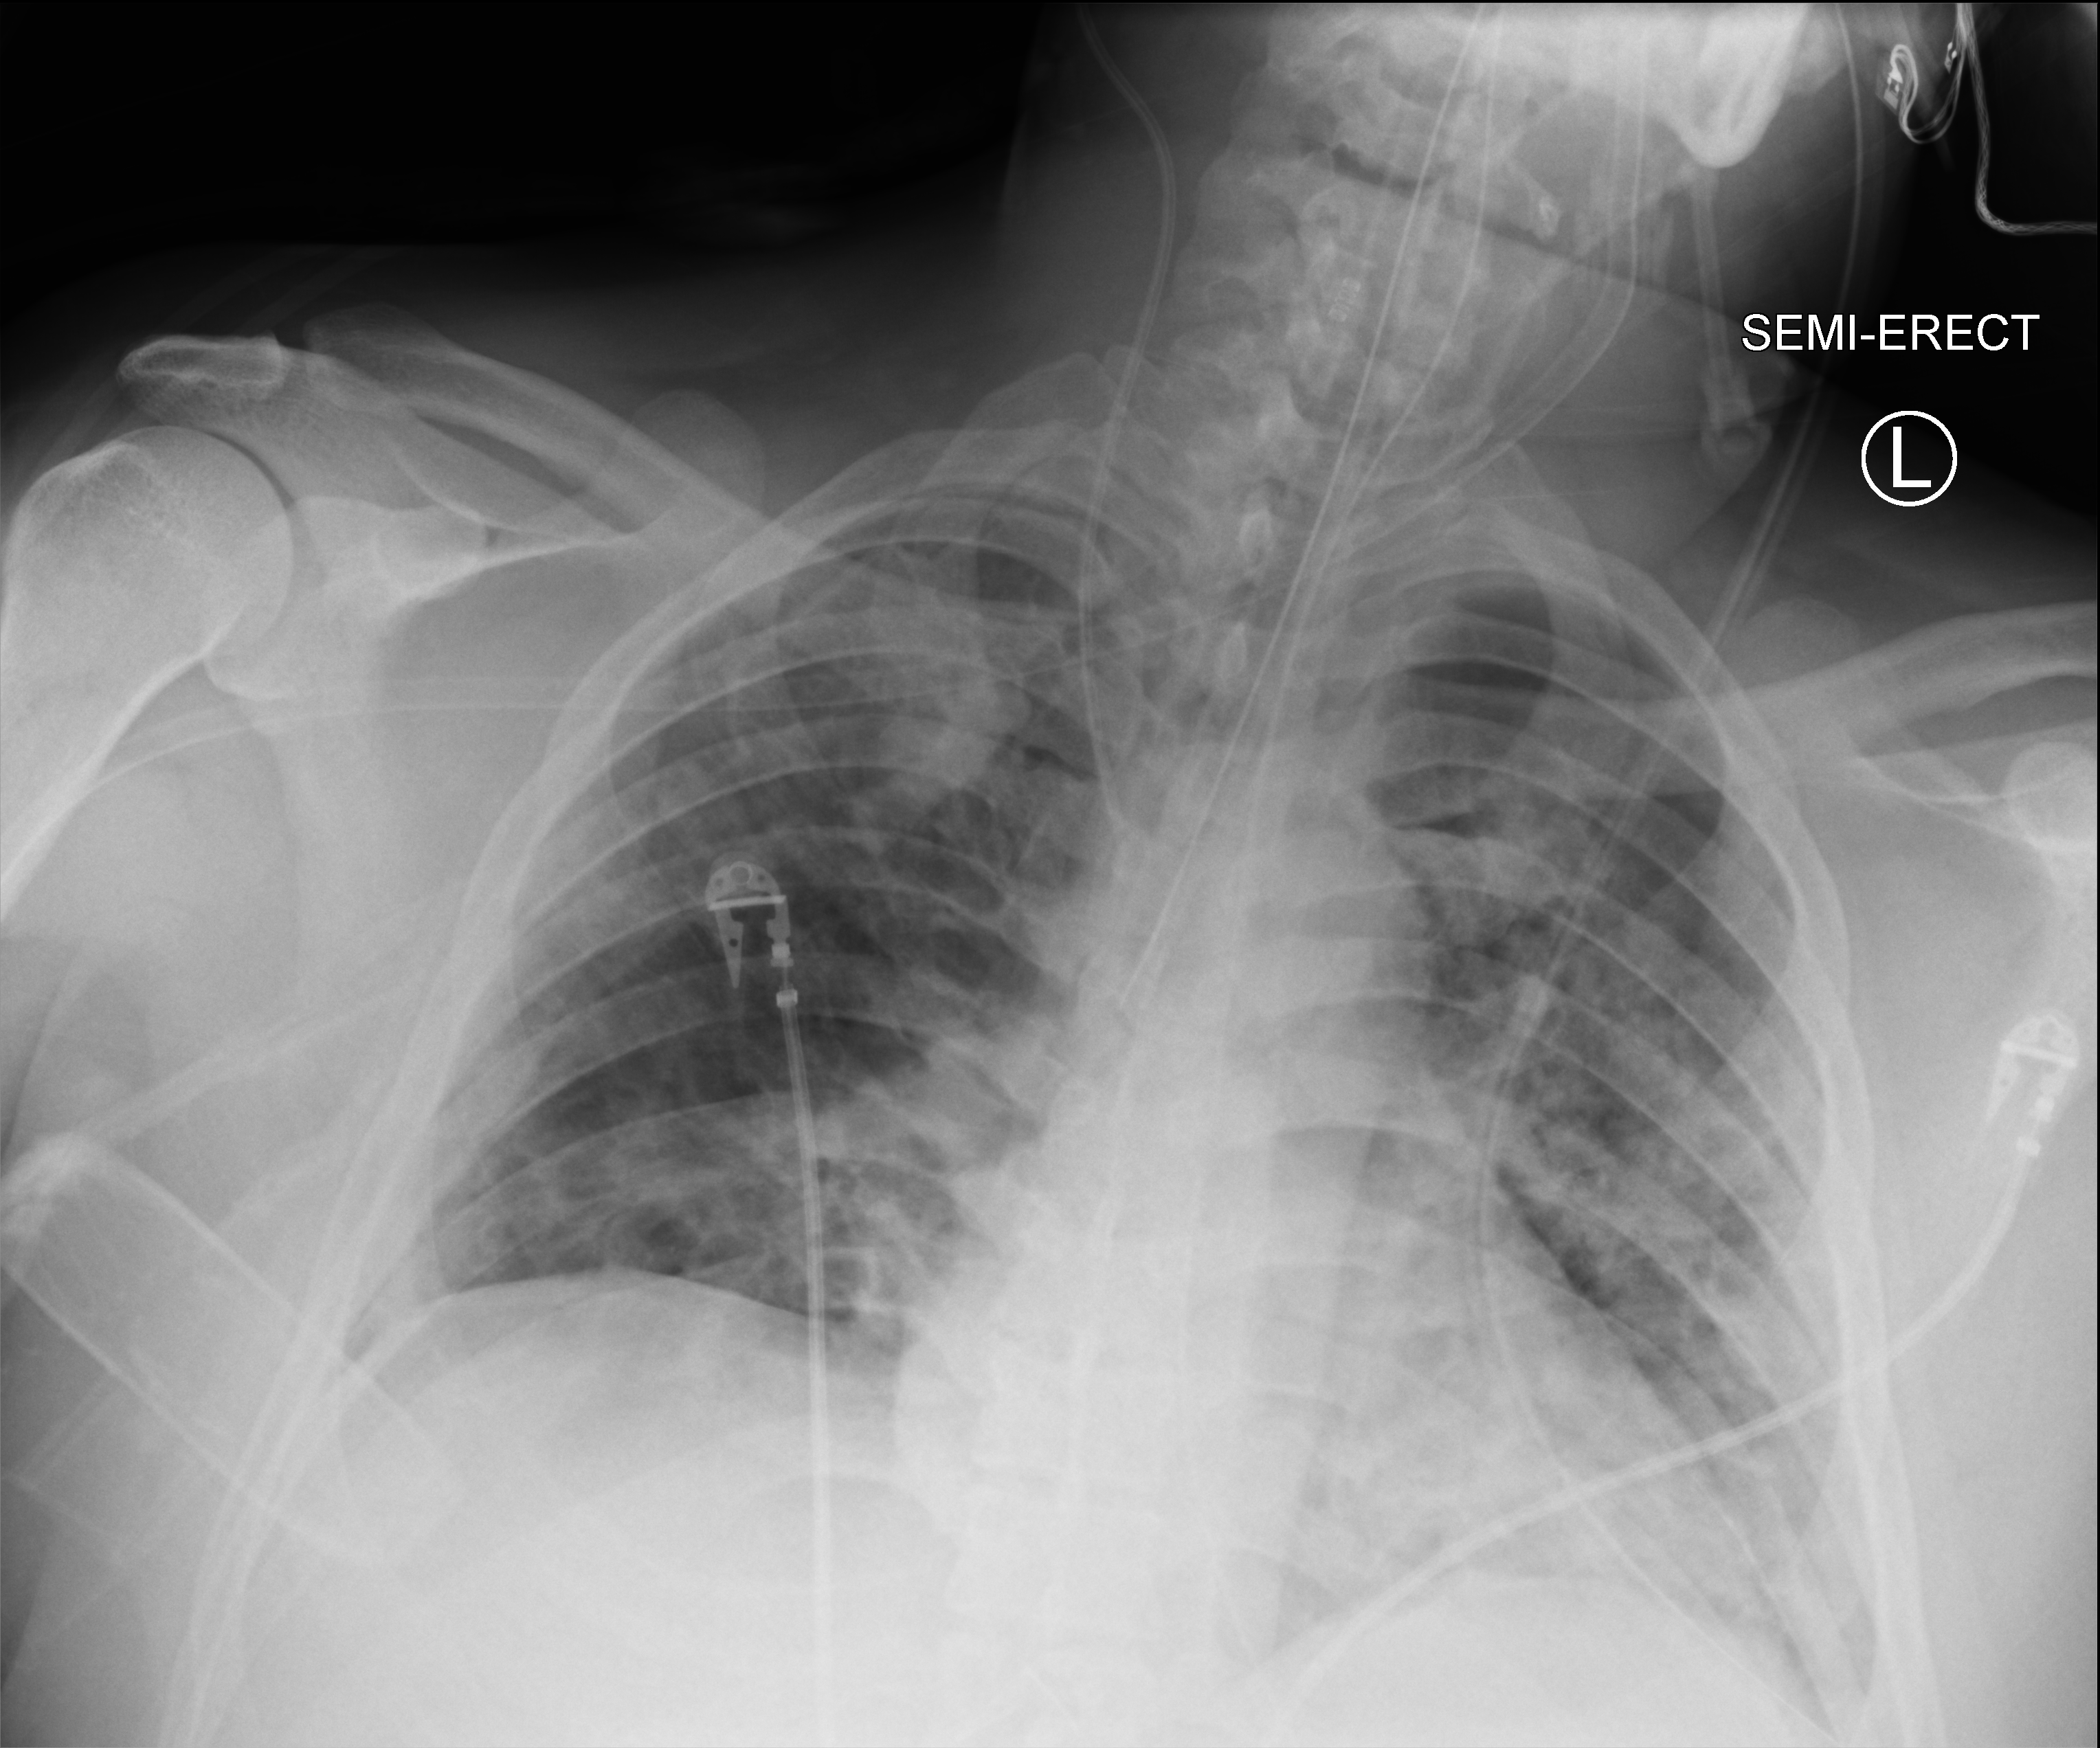
Bedside chest radiograph (computed radiography), anteroposterior (AP) projection. Male patient hospitalised with COVID-19, age 18–59 years.
Hospital-stay facts (about this admission, not read from this image; timing relative to this image not recorded): mechanically ventilated during this hospital stay: yes.